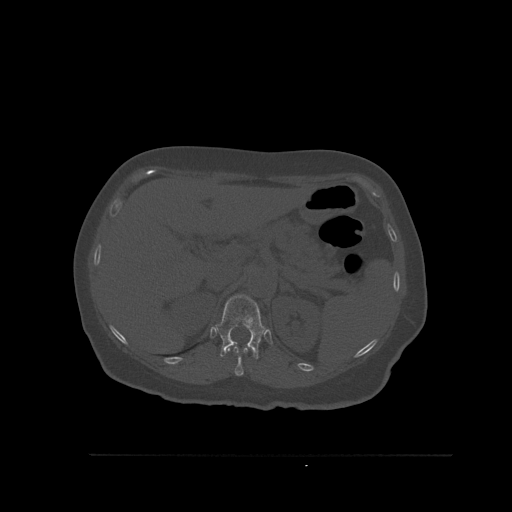
CT including the spine, one axial slice; position 290 of 527 along the scan axis; bone window (W 1800 / L 400 HU); 1.5 mm slice thickness; 512 × 512 image matrix, field of view 470 × 470 mm. Patient: female, 73 years. From the clinical record (not read from this slice): primary cancer: breast; vertebrae with lytic lesions (as recorded): L2.
Annotated regions visible in this slice (semi-automatically segmented with operator editing):
- T11 vertebra: bounding box [x1, y1, x2, y2] px = [226, 346, 248, 376]
- T12 vertebra: [215, 294, 265, 359]